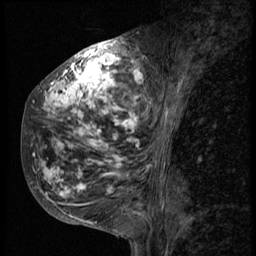
Breast MRI (dynamic contrast-enhanced), one sagittal slice. 3 images stored at this slice position (order not interpretable as contrast timing). 1.5 T. TE 4.2 ms, TR 9 ms. 256 × 256 image matrix, field of view 180 × 180 mm. Female patient, age 50 years. Case-level facts recorded for this patient, not image findings: setting: breast cancer imaged before/during neoadjuvant chemotherapy; receptor status: triple-negative.
Annotated regions visible in this slice (semi-automatic segmentation, software-assisted and operator-edited):
- analysis volume of interest (the breast-tissue region the enhancement analysis was run in; not a lesion): bounding box (x1, y1, x2, y2) in pixels: (23, 48, 169, 214)
- tumour enhancement mask (voxels above the 140 % enhancement threshold inside the analysis volume of interest): (33, 51, 169, 213)